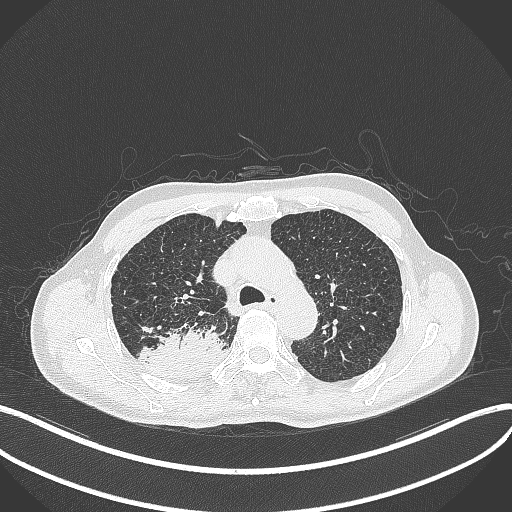
Chest CT, one axial slice. Reconstruction kernel B70f. Lung window (W 1500 / L -600 HU). 1 mm slice thickness. 512 × 512 image matrix, field of view 400 × 400 mm. Patient: male, 79 years. Case-level facts recorded for this patient, not image findings: clinical TNM (as recorded): T3 N0 M0.
Annotated regions visible in this slice (bounding box drawn by a radiologist):
- lung tumour (recorded histology: adenocarcinoma): bounding box (x1, y1, x2, y2) in pixels: (139, 322, 230, 382)